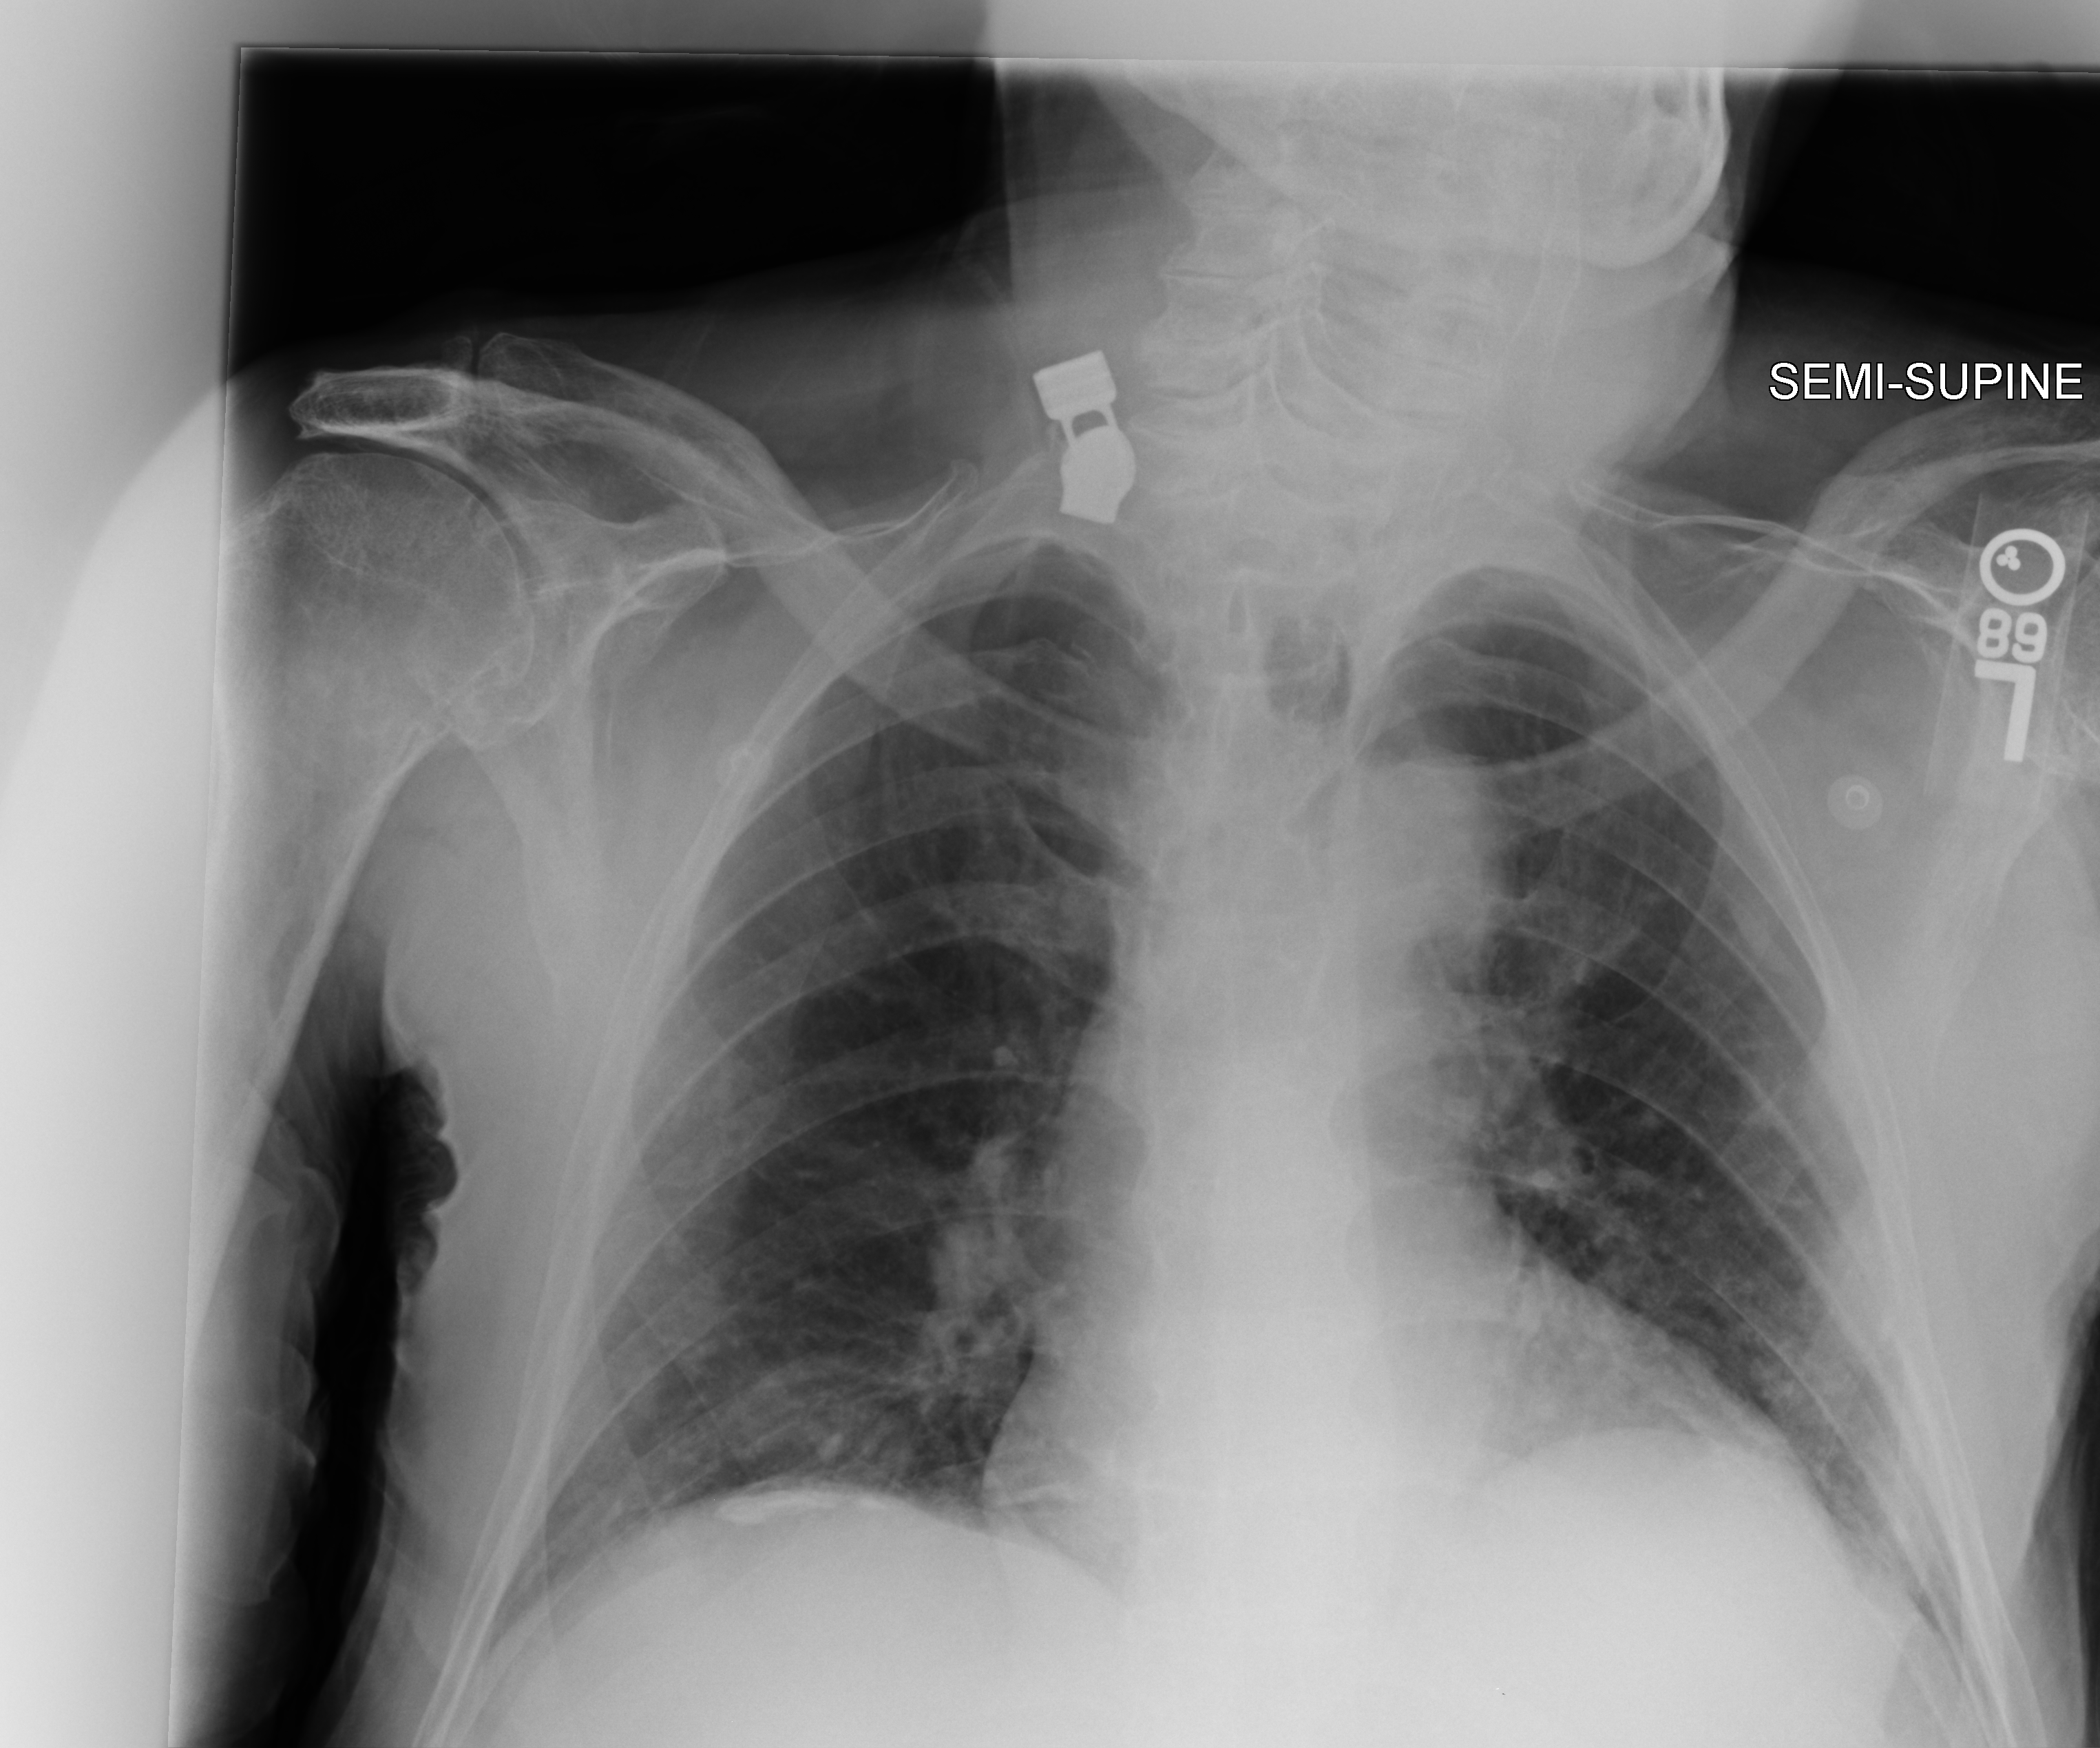
Bedside chest radiograph (computed radiography), anteroposterior (AP) projection. Male patient hospitalised with COVID-19, age 75–90 years.
From the hospital-stay record, not from the radiograph (when in the stay this image was taken is not recorded):
- admitted to intensive care during this hospital stay: no